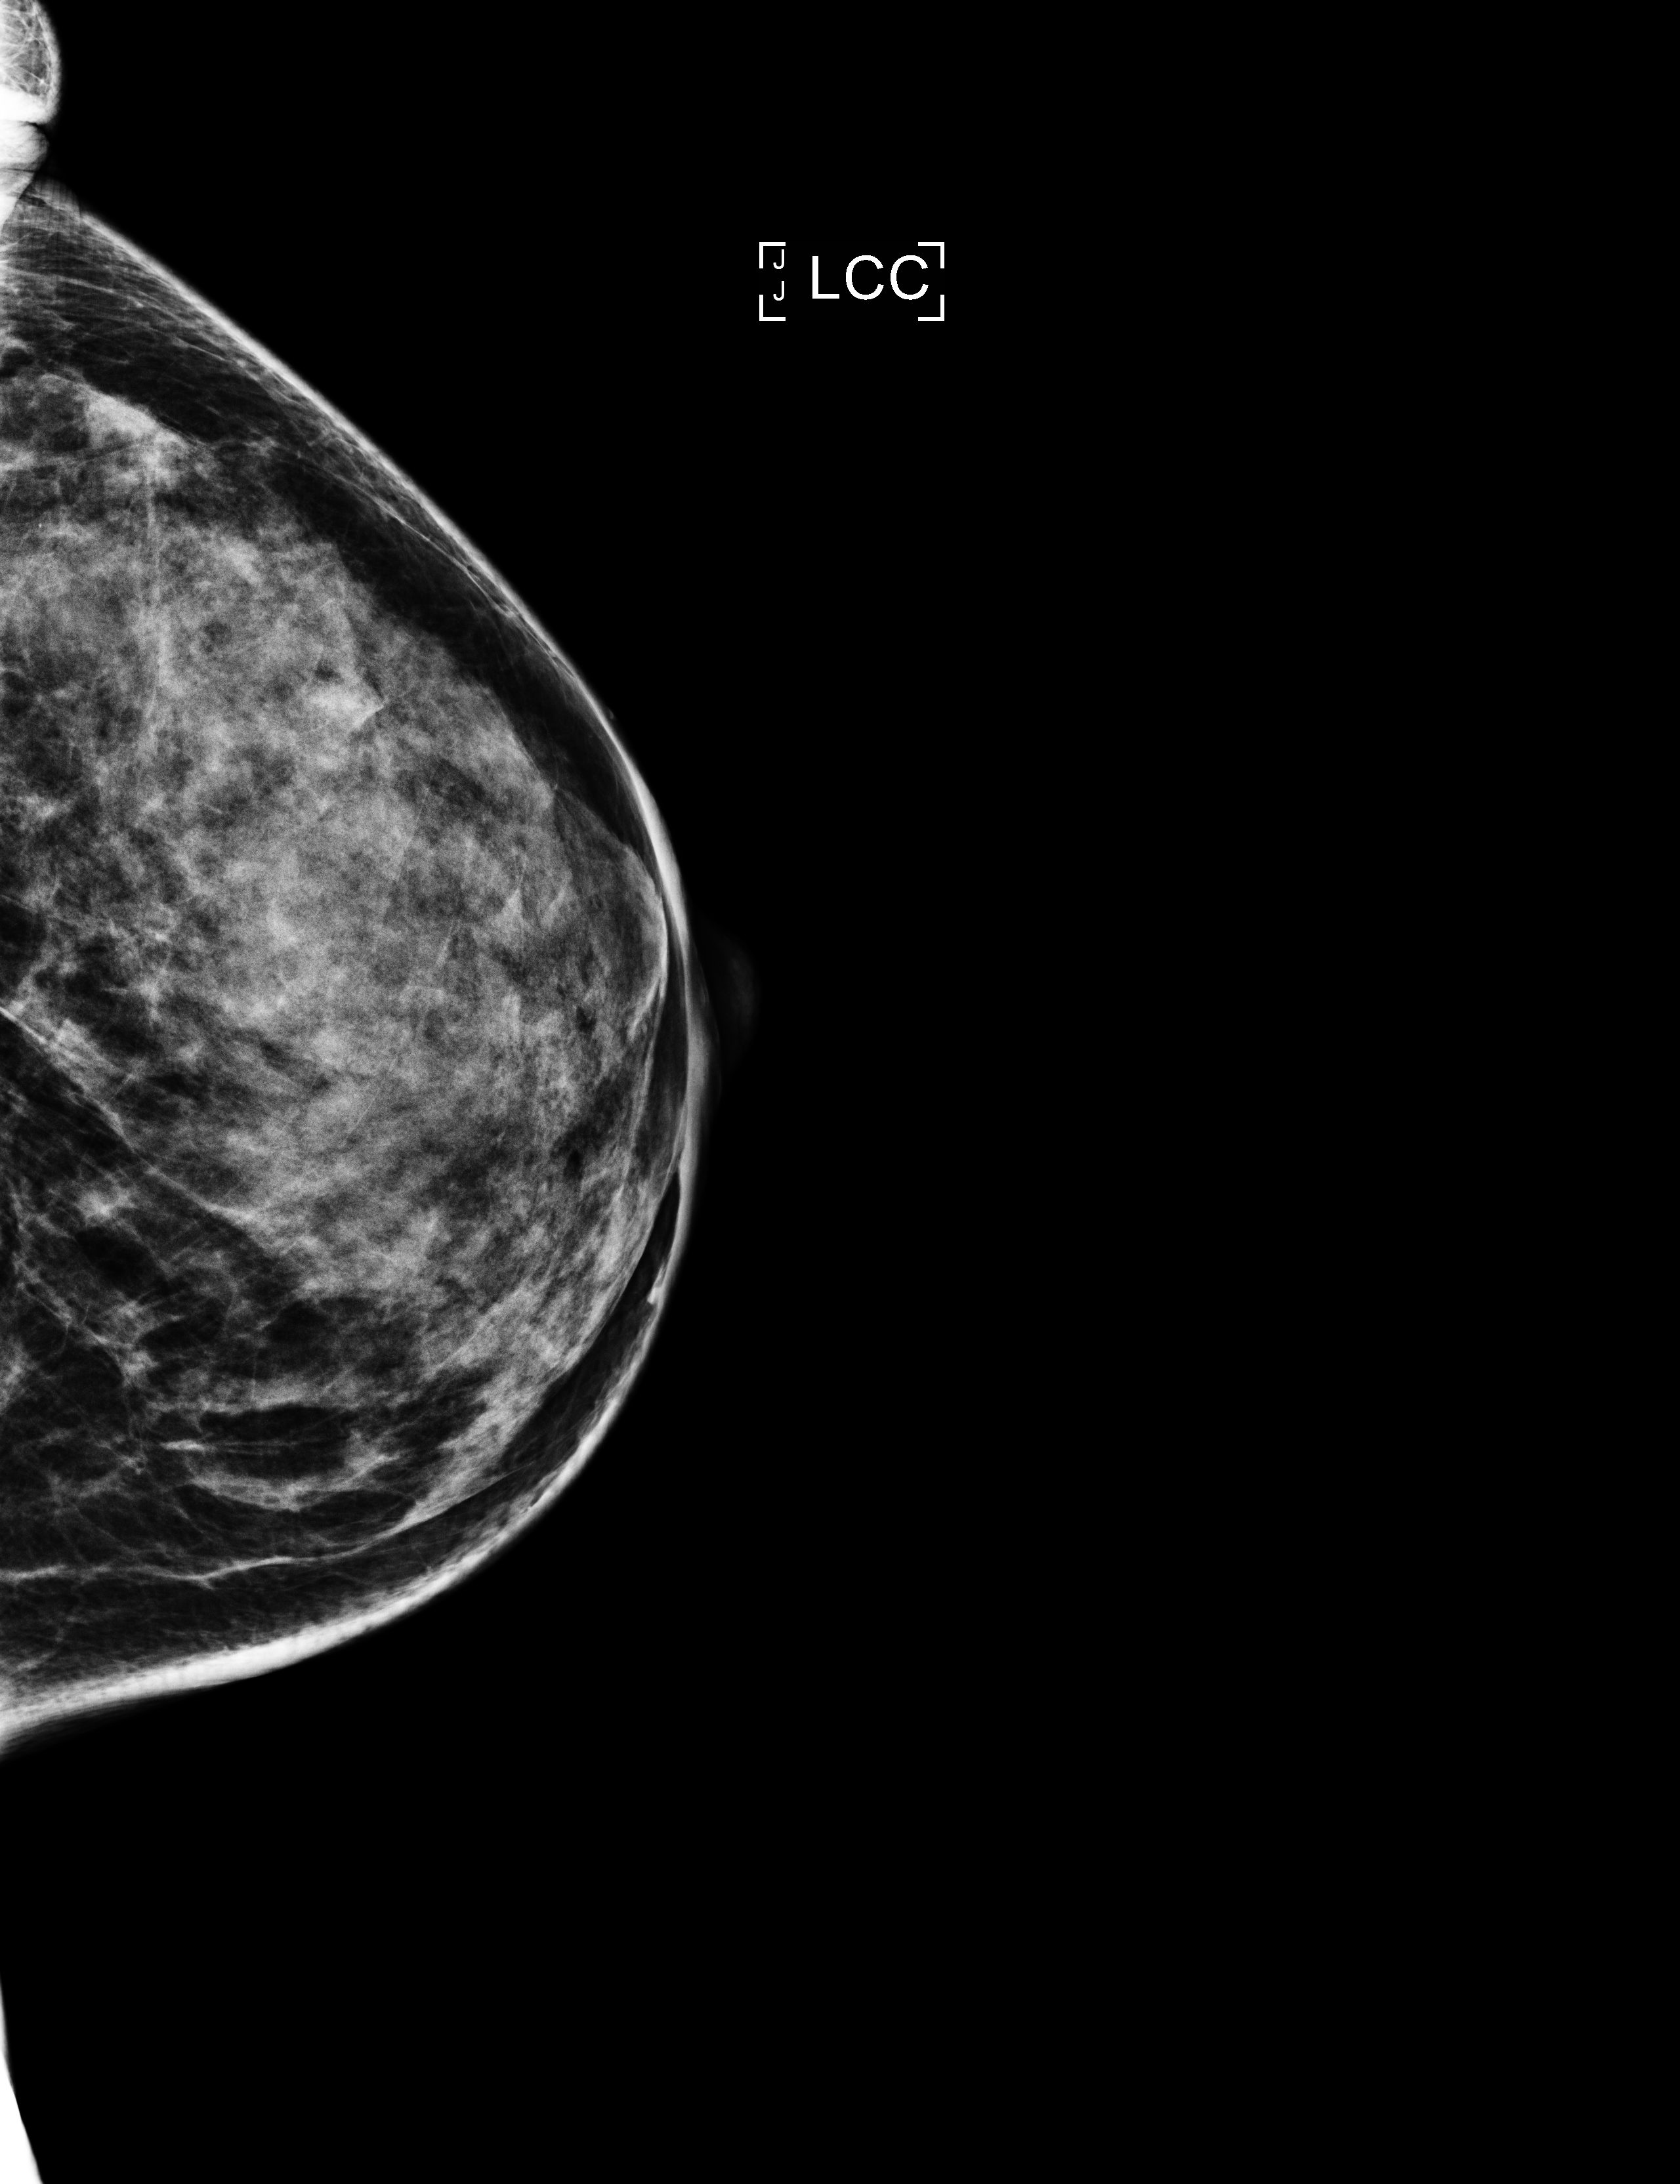
Digital mammogram (FFDM), left breast, craniocaudal (CC) view, annual screening mammography examination, compressed breast thickness 54 mm, system: Selenia Dimensions. Patient: female, 43 years.
Breast density at the screening exam (both breasts): extremely dense (BI-RADS density category d). Final BI-RADS assessment for this screening round (tomosynthesis exam, both breasts): category 1. Recall: no recall after this screen.